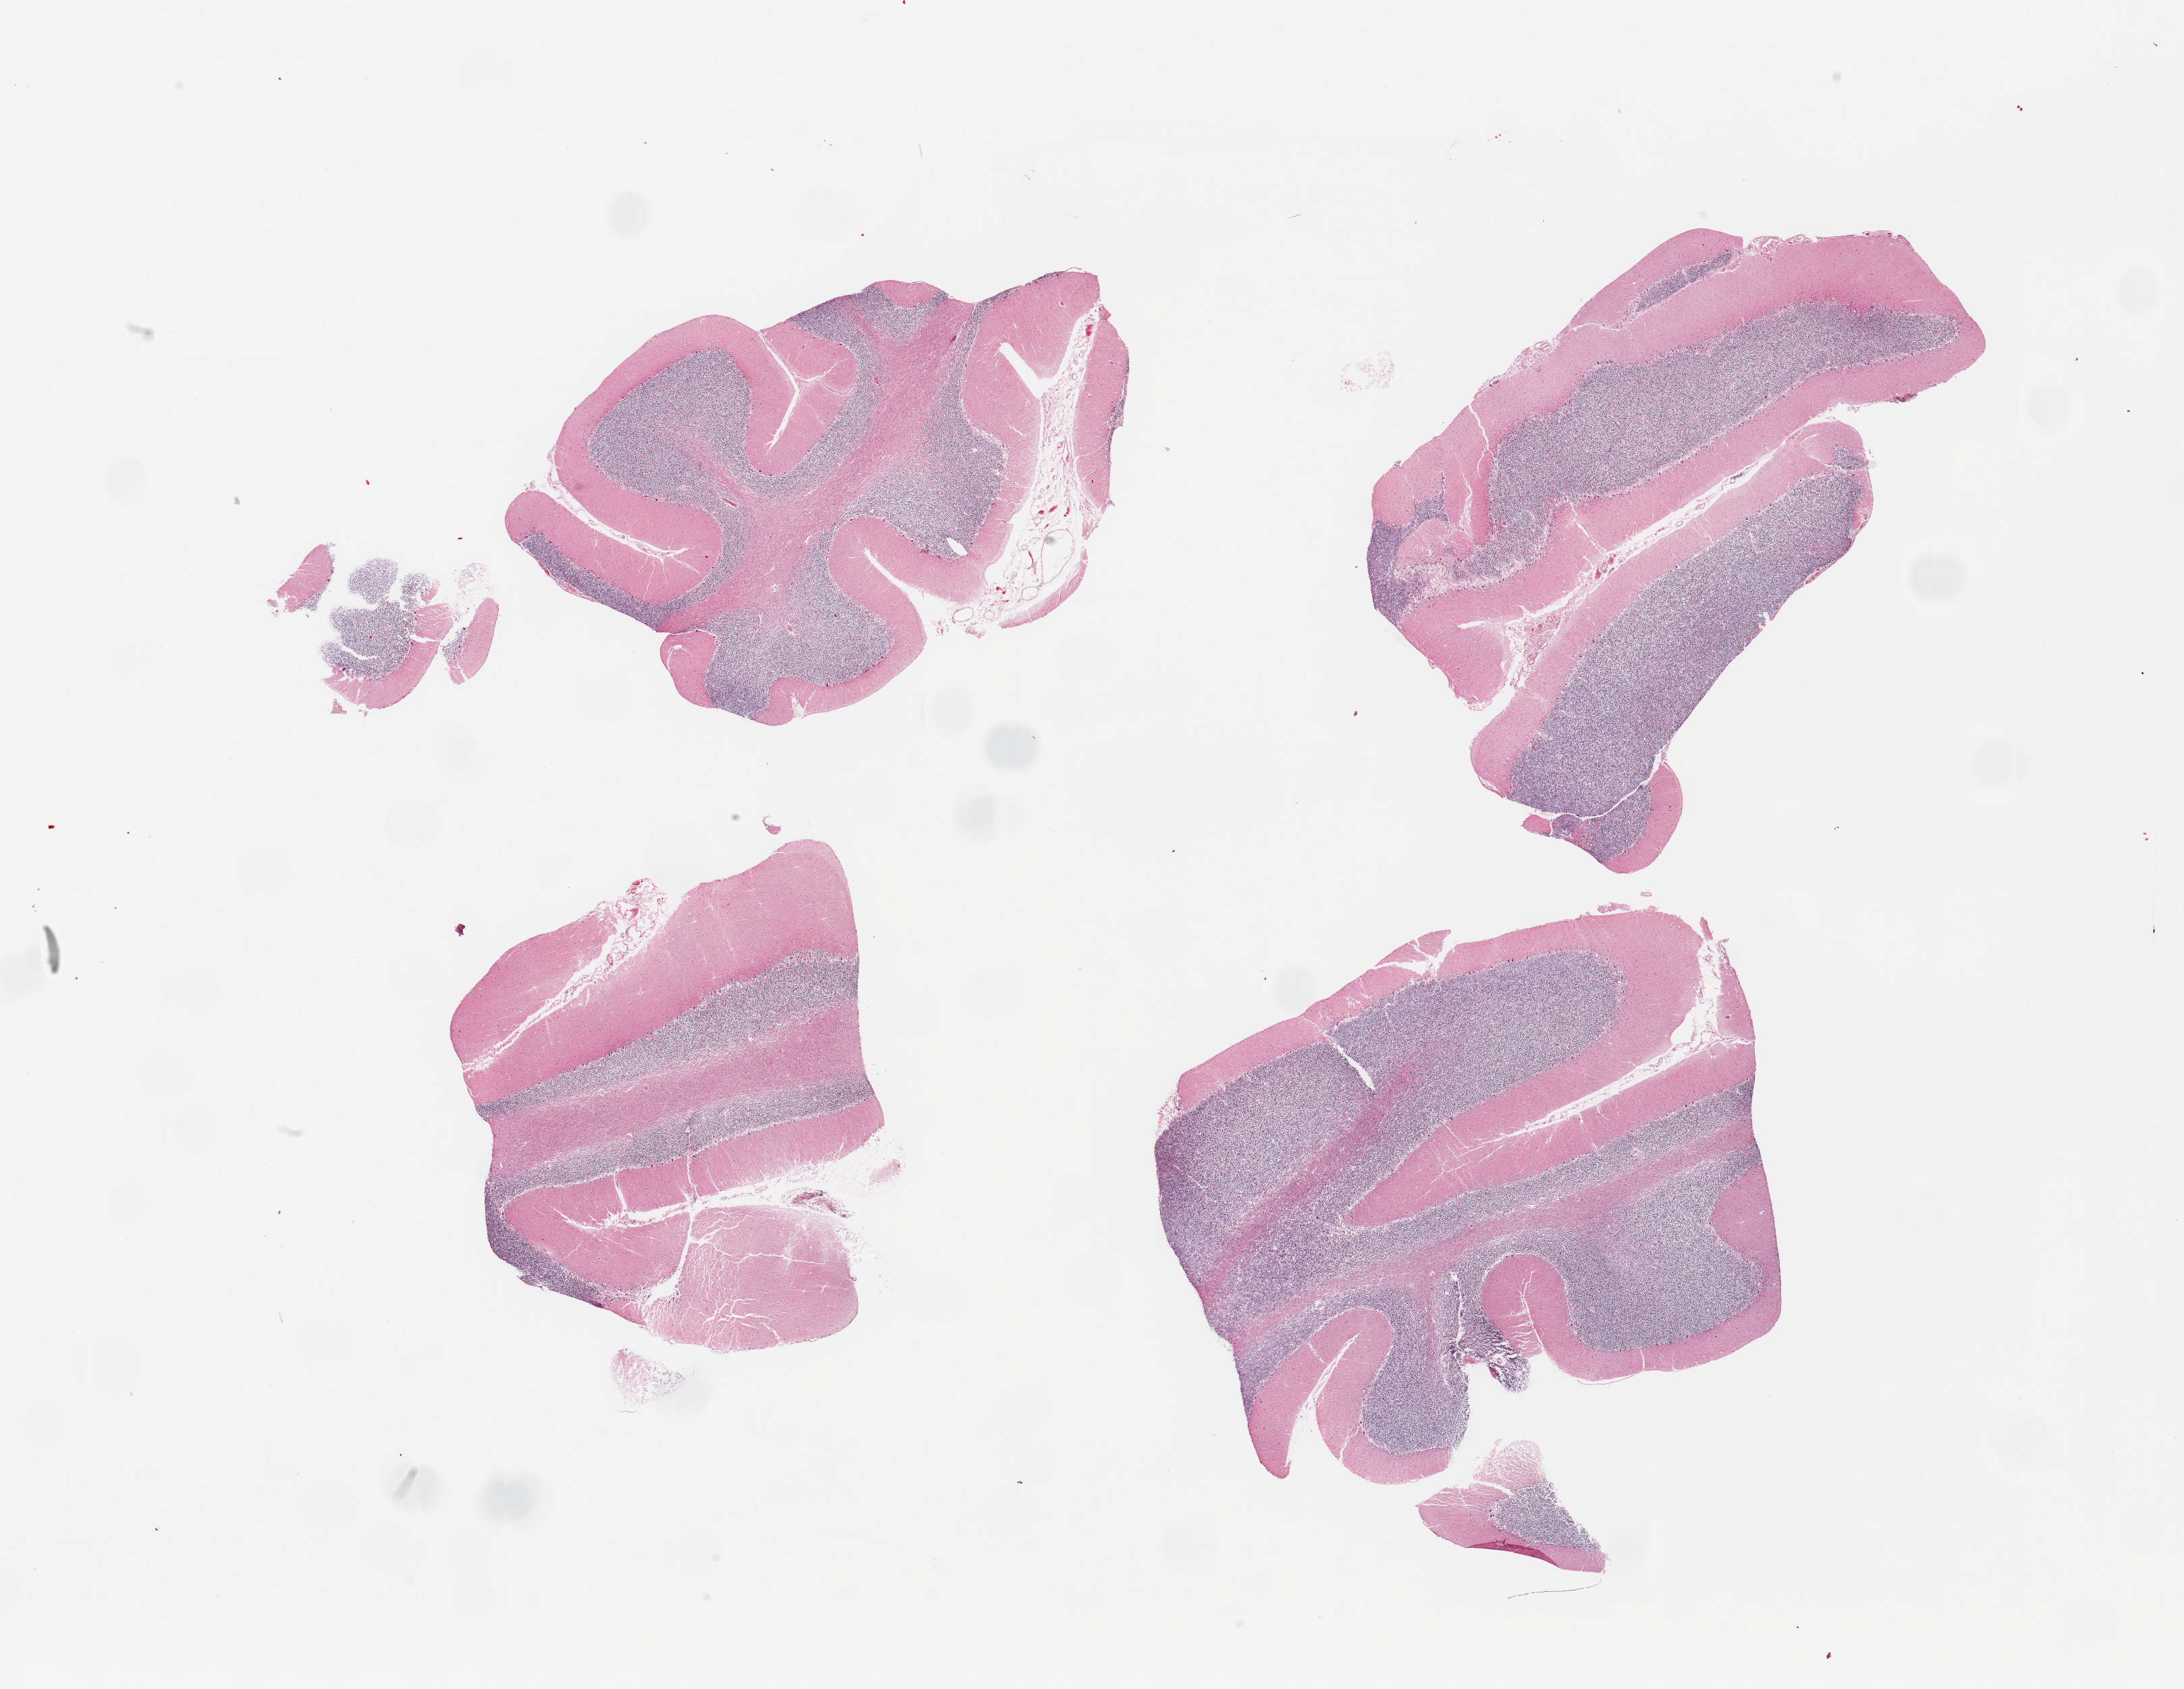
Haematoxylin and eosin whole-slide image, low-resolution overview of the scanned area, about 25.6 x 19.8 mm. PAXgene-fixed paraffin-embedded (PFPE) section. Sampled site (target tissue): cerebellum. Donor tissue sample. Donor: male.
Review note (as recorded): 4 pieces no abnormalities.